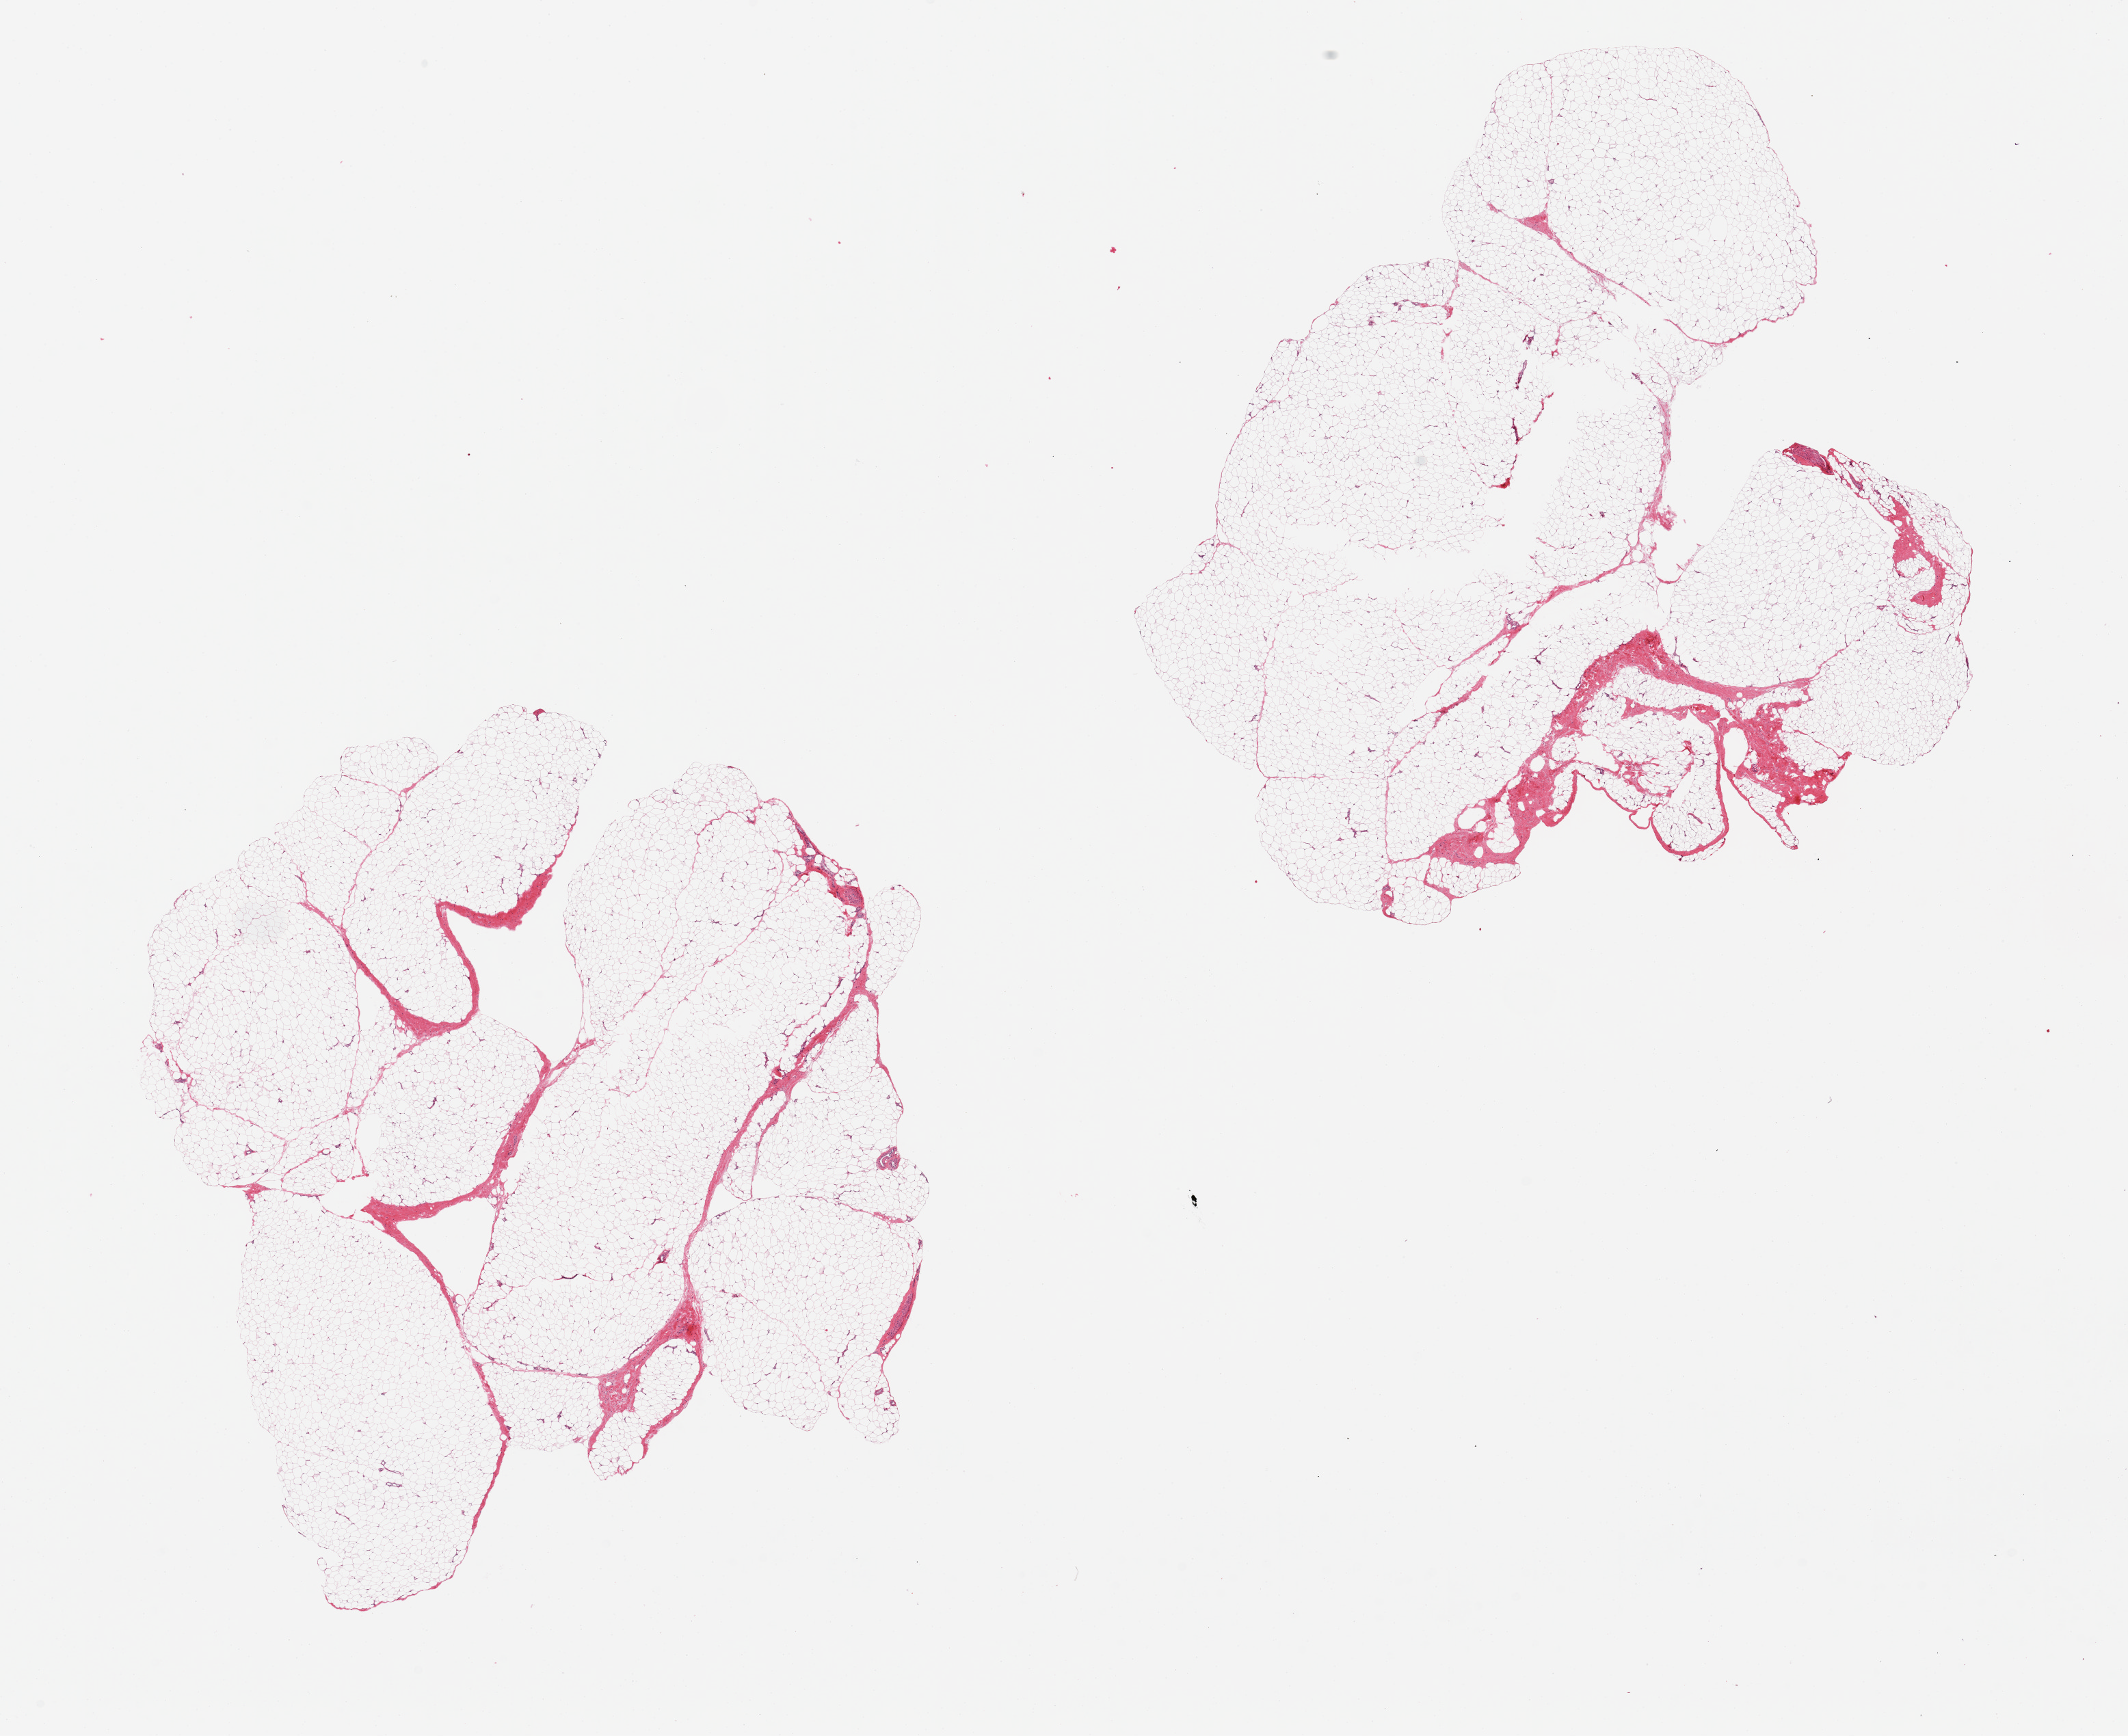
Haematoxylin and eosin whole-slide image — low-resolution overview of the scanned area, about 24.6 x 20.1 mm (slide scanned at 20x), PAXgene-fixed paraffin-embedded (PFPE) section, target tissue: adipose tissue, tissue donor sample. Male donor.
Review note (as recorded): 1 pieces, ~10% fibrous tissue.